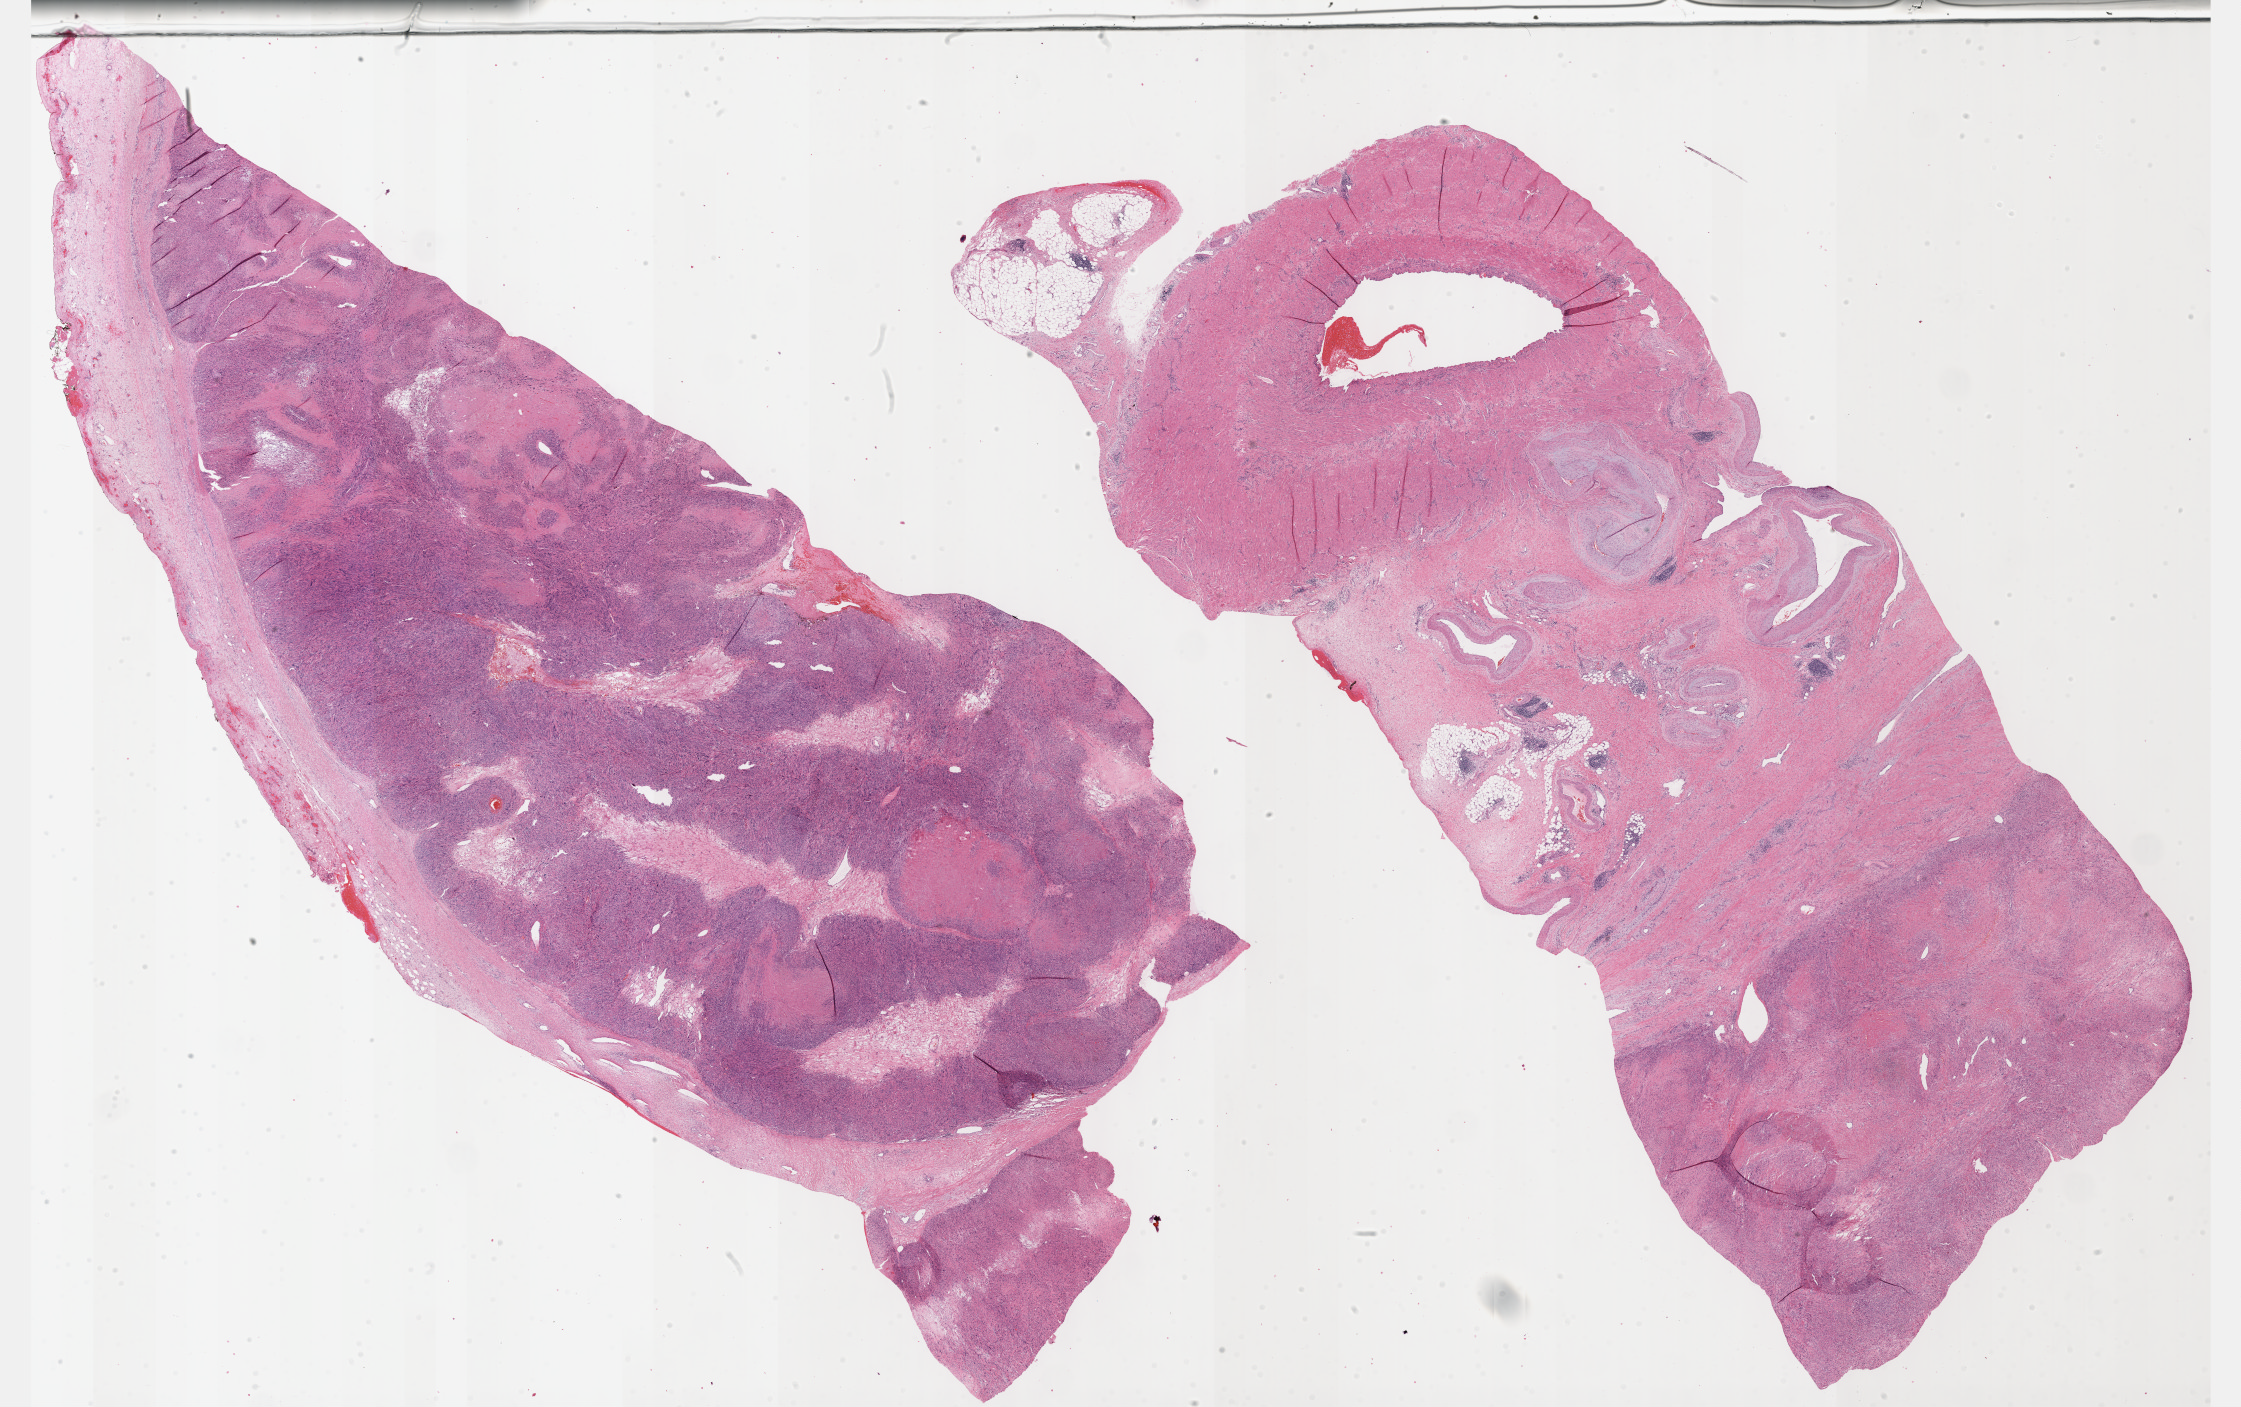
Digitized H&E-stained tissue section (whole slide), shown as a low-resolution overview of the whole scanned area (about 36.2 x 22.7 mm, acquisition: 40x scan), formalin-fixed paraffin-embedded (FFPE) diagnostic section, retroperitoneum and peritoneum, primary tumour sample. Patient: female, age at initial diagnosis 63 years.
Histologic diagnosis: Leiomyosarcoma, NOS.